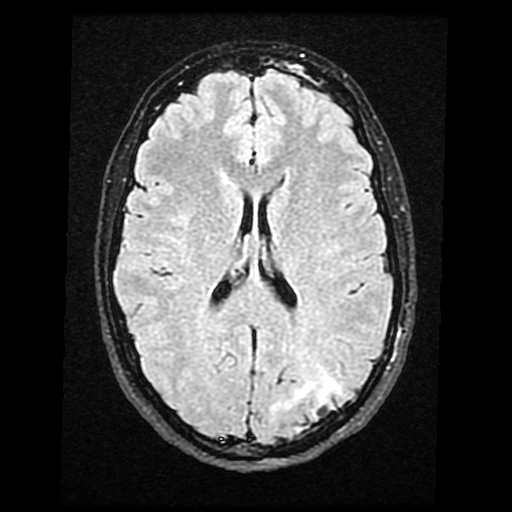
Brain MRI from a brain-tumour surgery series, one axial slice. T2 FLAIR. 4 mm slice thickness. 512 × 512 image matrix. Case-level facts recorded for this patient, not image findings: histopathology: Glioma with ependymal features; WHO grade: 2; tumour location: Left Parietal.
Outlined on this slice (outlined manually by an expert reader):
- tumour: box from (x=271, y=365) to (x=339, y=433) px